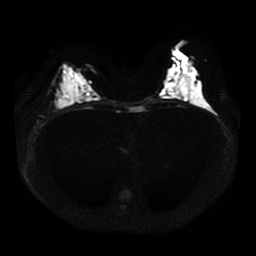
Breast MRI, one axial slice; slice 22 of 41 in the series (ordered by position); diffusion-weighted series; image 2 of 4 stored at this slice position (different b-values; order by instance number); 1.5 T; 5 mm slice thickness; 256 × 256 image matrix. Female patient.
Outlined on this slice (expert manual segmentation):
- tumour on diffusion-weighted imaging: bounding box <59,99,70,107> (left, top, right, bottom; pixels)